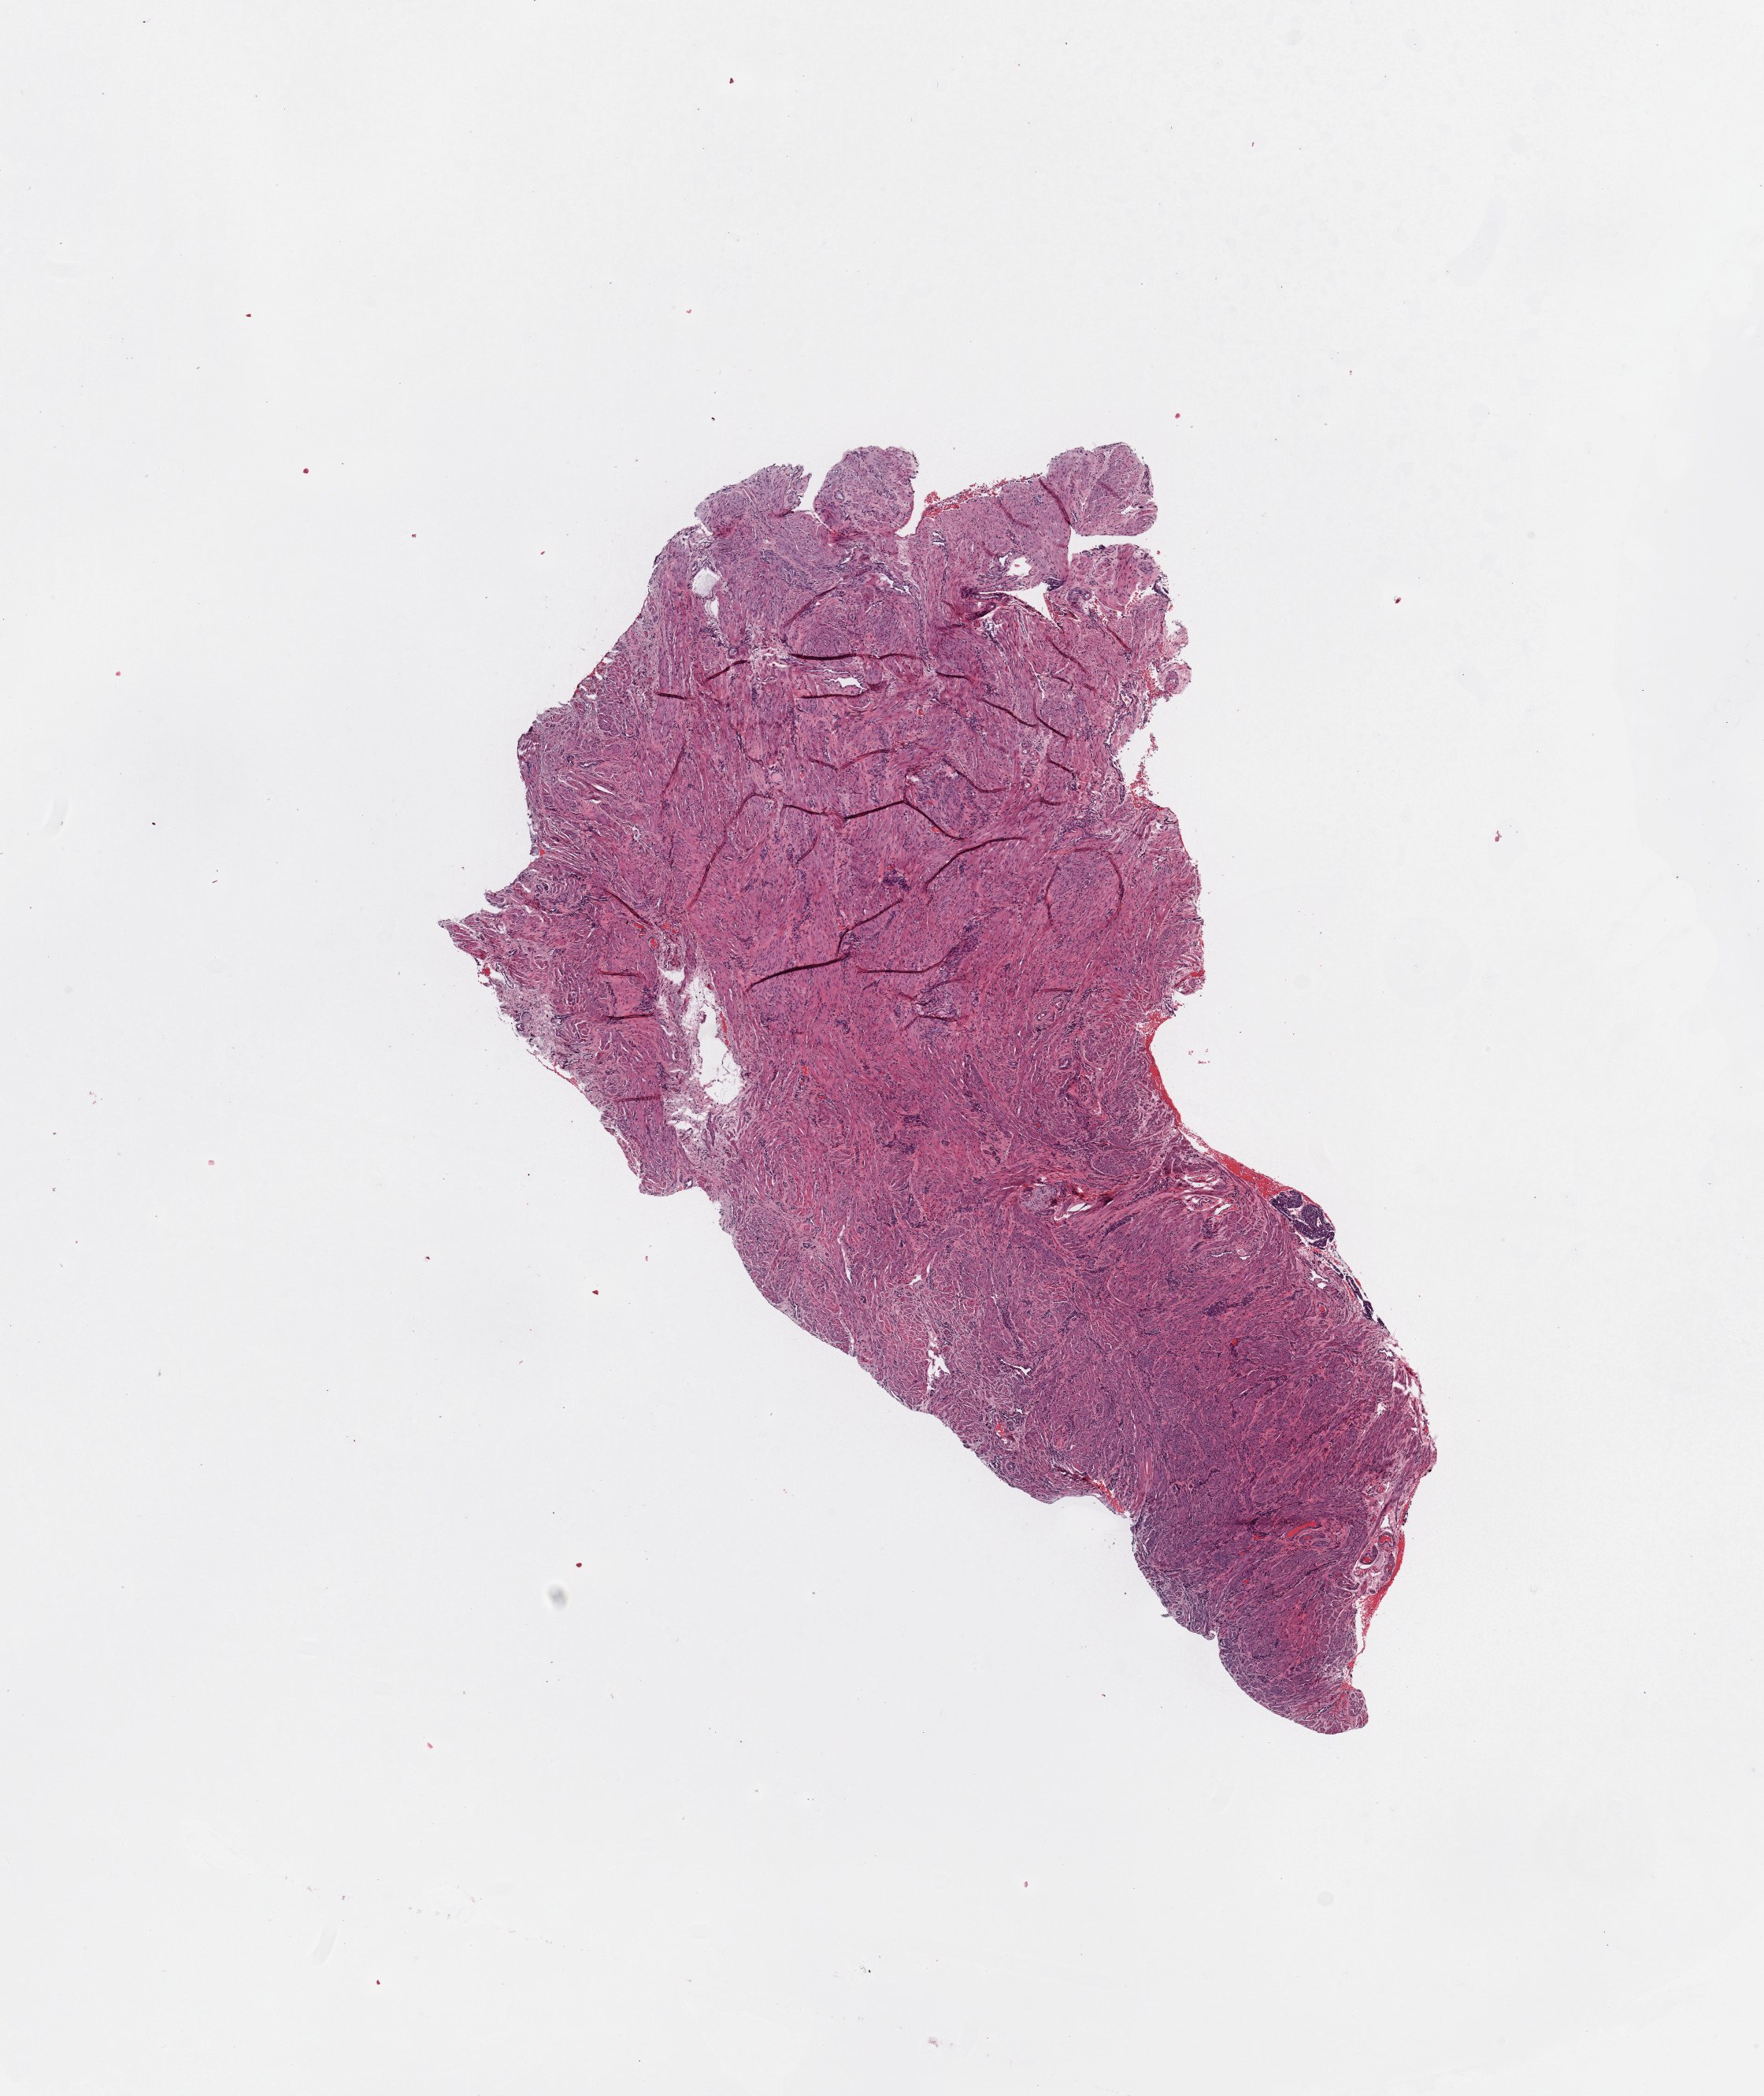
Digitized H&E tissue section (whole slide) — shown as a low-resolution overview of the whole scanned area (about 8.9 x 10.5 mm, from a 20x scan); normal (non-tumour) tissue sample, uterus. Female, 48 y/o.
This section: normal (non-tumour) tissue from the same patient. Patient diagnosis: Endometrioid adenocarcinoma, NOS.